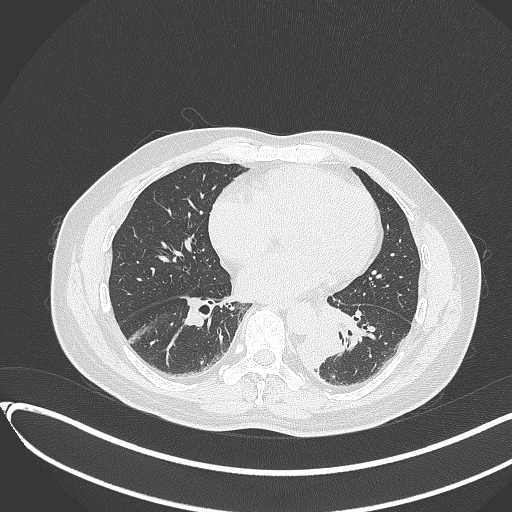
Chest CT, one axial slice. Position 136 of 417 along the scan axis. Reconstruction kernel B70f. 120 kVp. Lung window (W 1500 / L -600 HU). 1 mm slice thickness. 512 × 512 image matrix. Male patient, age 54 years. From the clinical record (not read from this slice): clinical TNM (as recorded): T3 N0 M0.
Structures marked on this image (rectangle marked by the reading radiologist):
- lung tumour (recorded histology: squamous cell carcinoma): box from (x=293, y=321) to (x=350, y=373) px